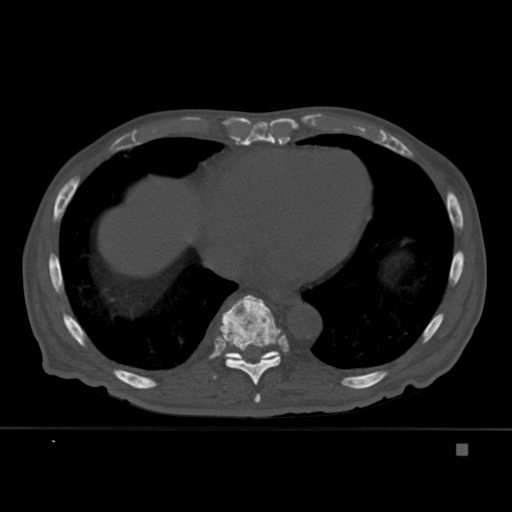
CT including the spine, one axial slice; slice 244 of 451 in the series (ordered by position); bone window (W 1800 / L 400 HU); 1.5 mm slice thickness; 512 × 512 image matrix. Male patient, age 75 years. Case-level facts recorded for this patient, not image findings: primary cancer: prostate.
Structures marked on this image (semi-automatic segmentation, software-assisted and operator-edited):
- T10 vertebra: bounding box (x1, y1, x2, y2) in pixels: (224, 351, 279, 359)
- T8 vertebra: (254, 394, 261, 403)
- T9 vertebra: (213, 295, 289, 386)